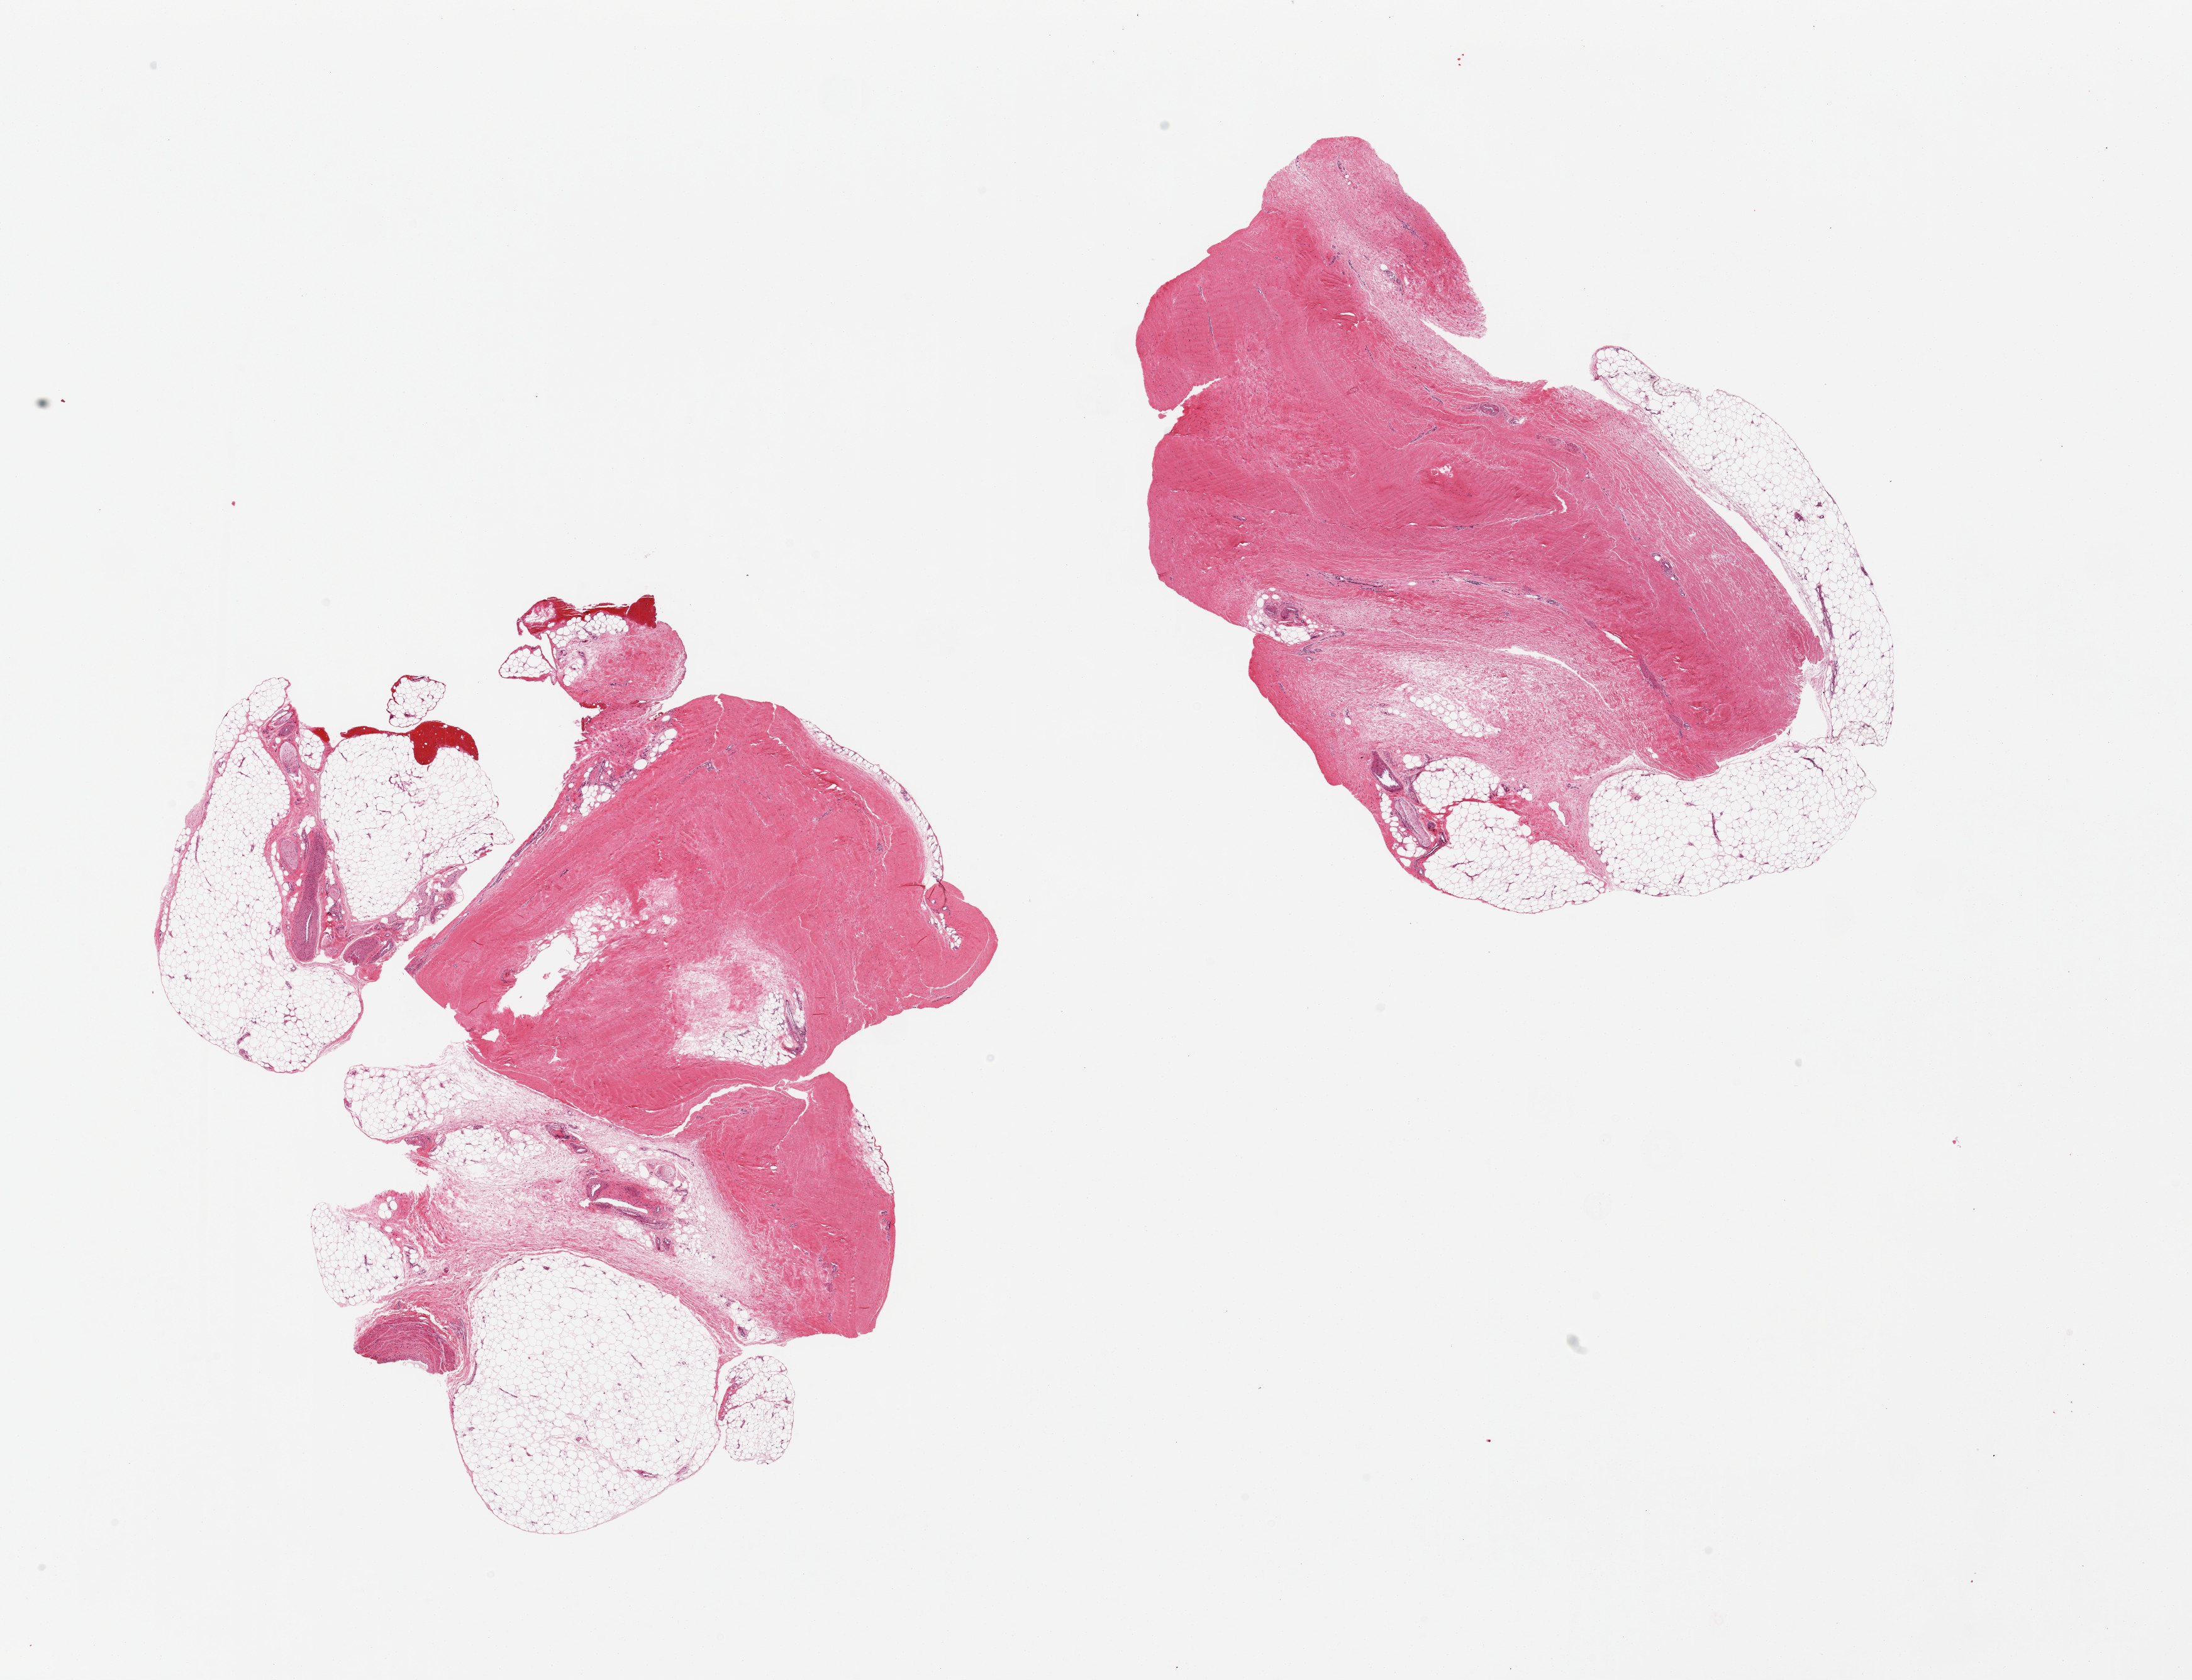
Digitized haematoxylin and eosin-stained section — a low-resolution overview of the entire scanned area, about 27.6 x 21.1 mm (acquisition: 20x scan); PAXgene-fixed, paraffin-embedded tissue; sampled site (target tissue): adipose tissue; tissue donor sample. Male donor.
• reviewer comment on this tissue sample: 2 pieces. Both pieces contain large amounts of dense fibrous tissue, probably fascia: 90% of 1 and 60% of other